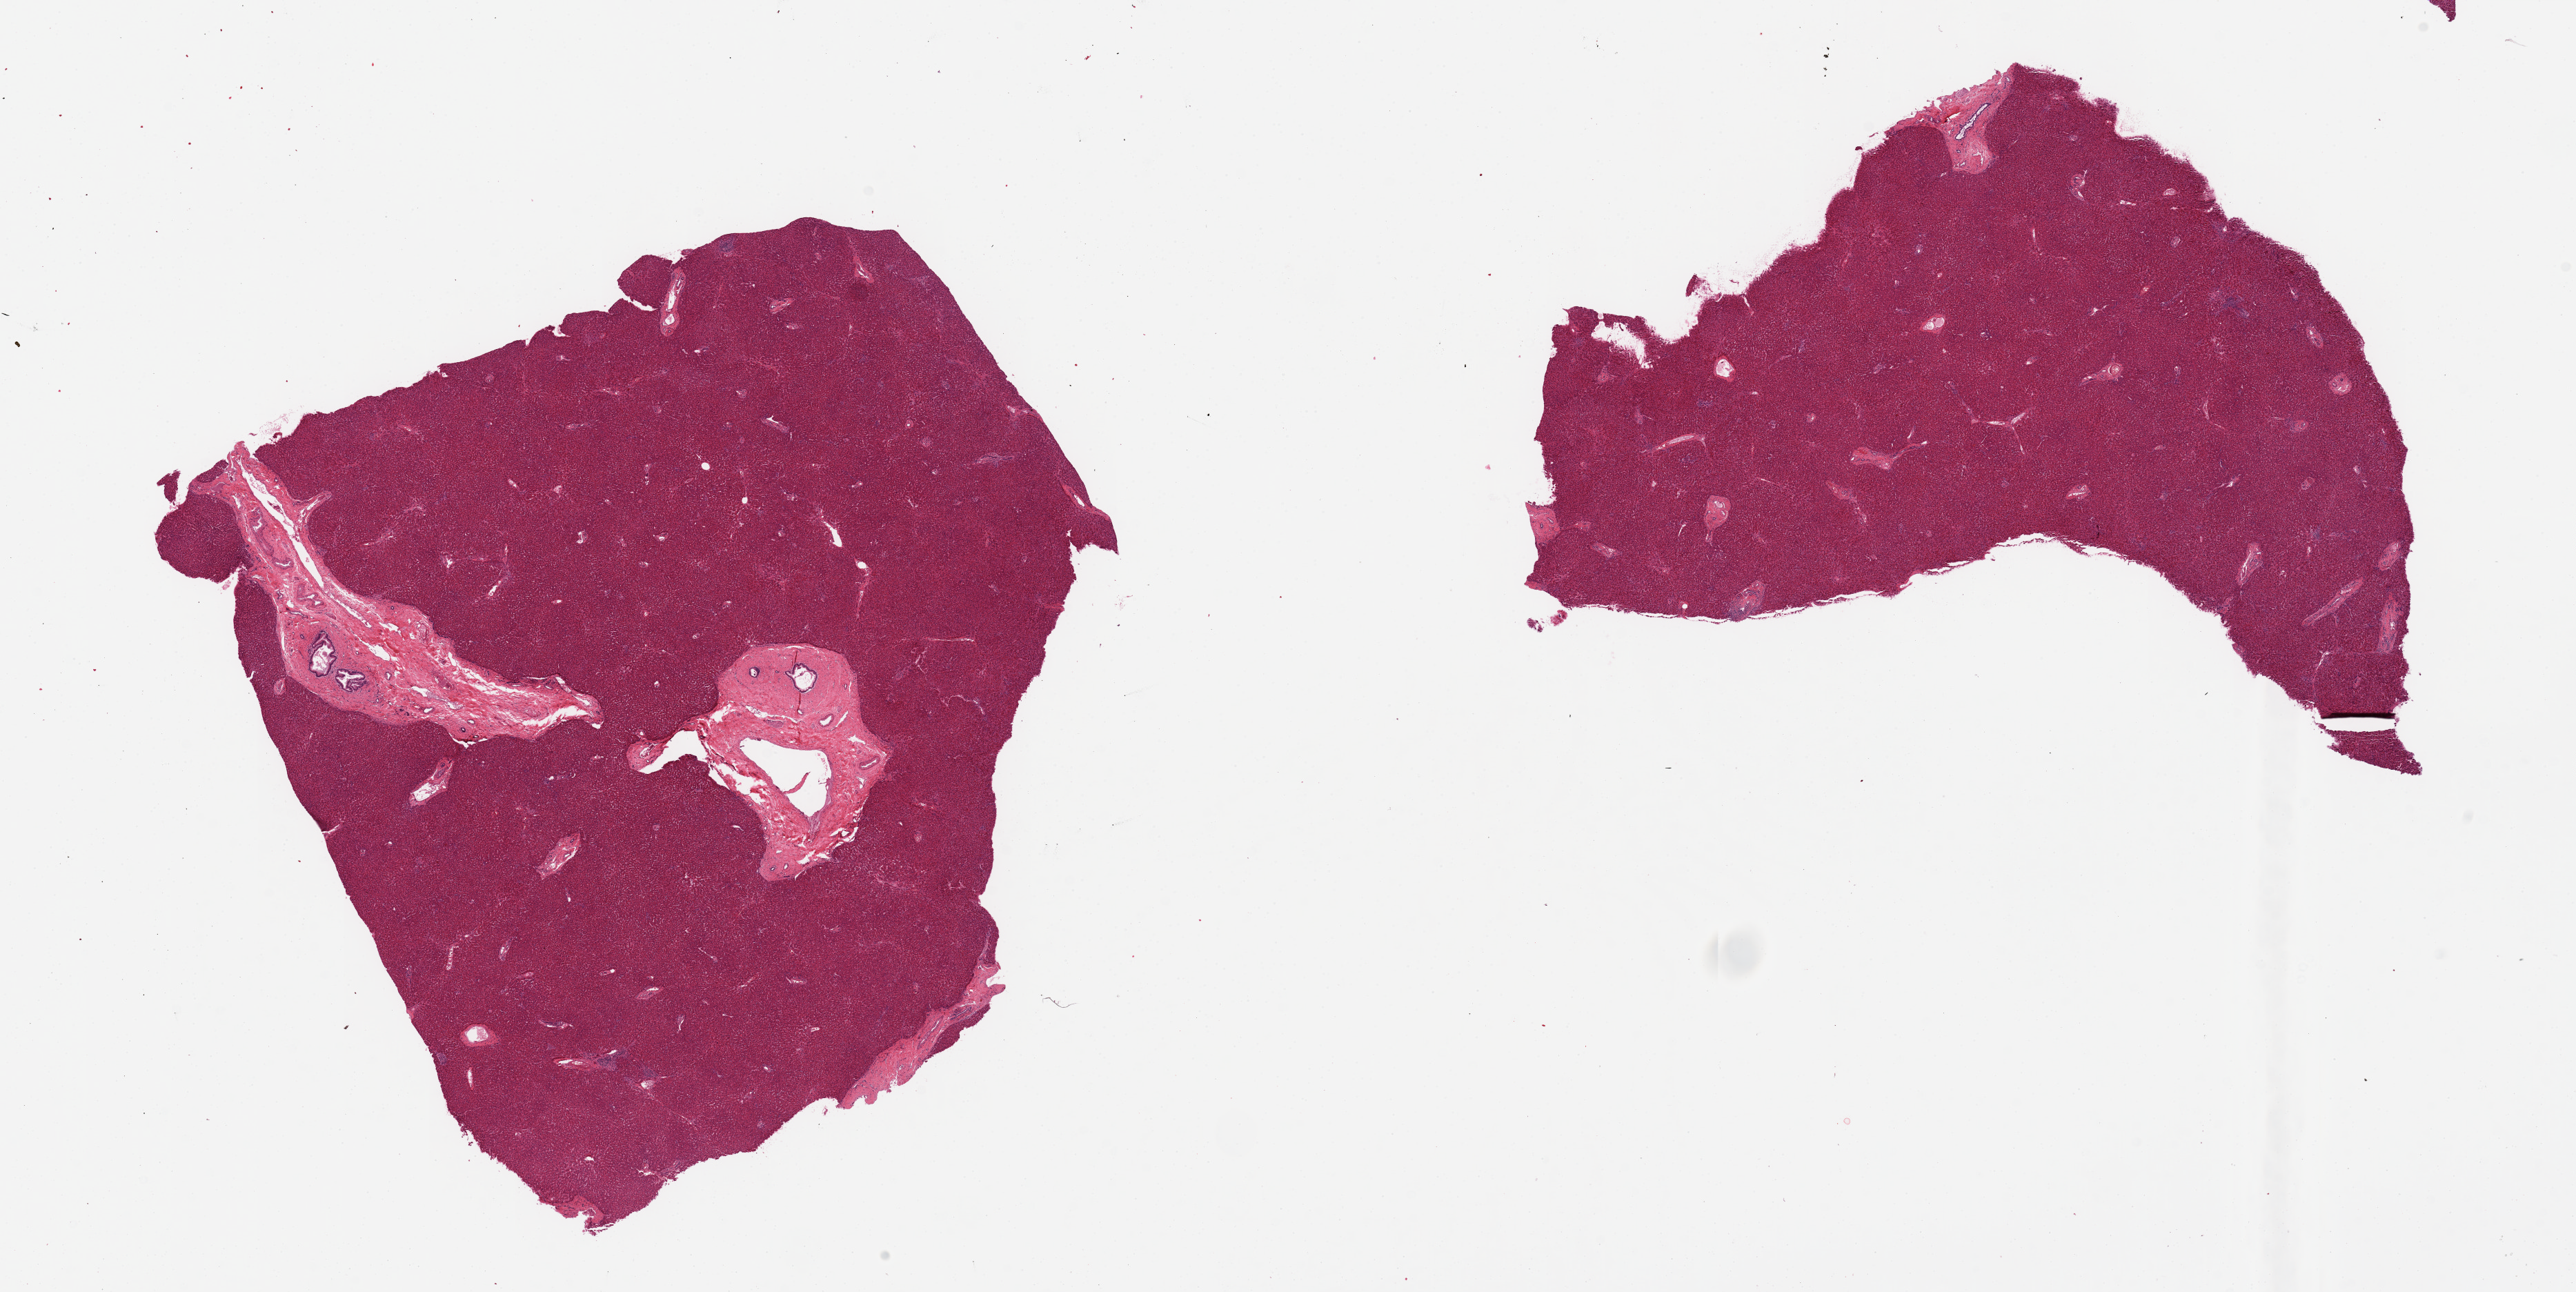
Digitized H&E-stained section, whole scanned area (about 29.5 x 14.8 mm) shown as a low-resolution overview, PAXgene-fixed paraffin-embedded (PFPE) section, sampled site (target tissue): liver, donor tissue sample. Female donor.
Pathologist's review note for this sample: 2 pieces, few collections of lymphocytes.